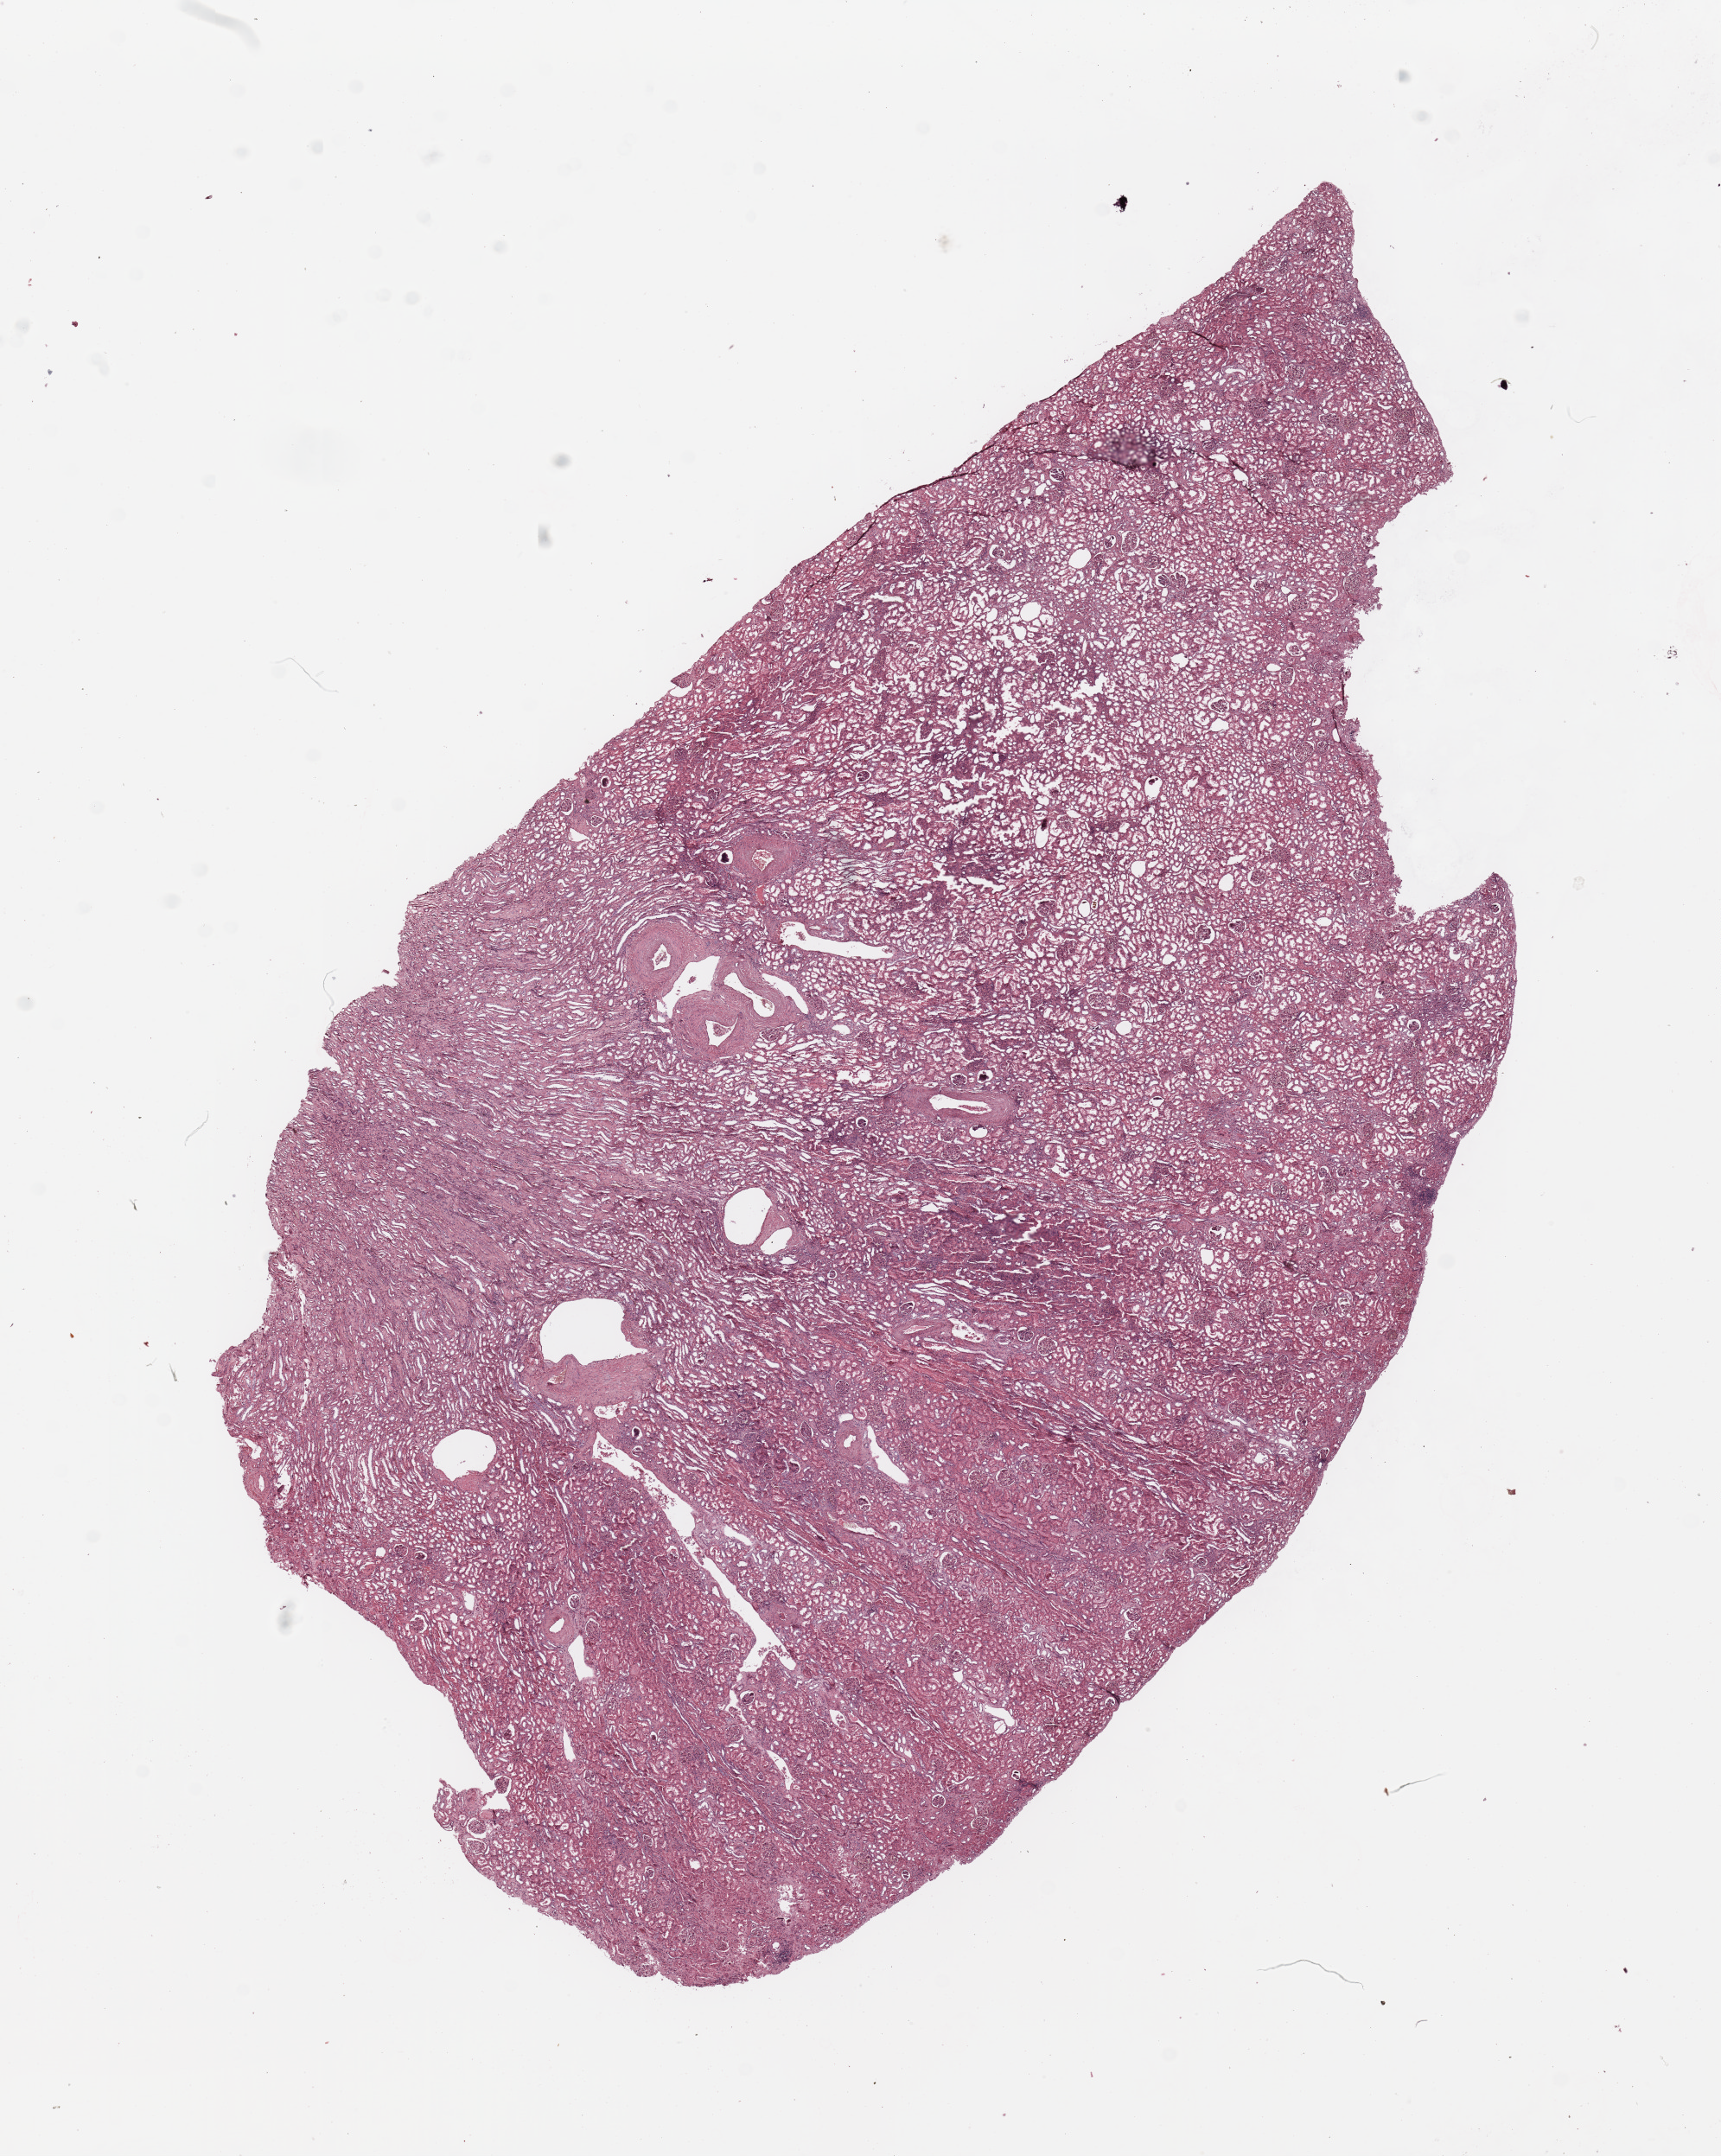
Hematoxylin and eosin (H&E) stained whole-slide image, low-resolution overview of the scanned area, about 15.8 x 19.7 mm. Patient: male, age 64 years.
• patient diagnosis (cohort enrolment): sarcoma (site not recorded at cohort level)